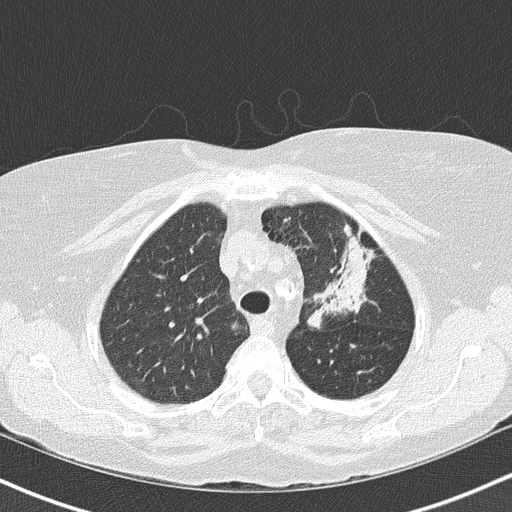
Low-dose screening chest CT, one axial slice; slice 117 of 147 in the series (ordered by position); reconstruction kernel B50f; lung window (W 1500 / L -600 HU); 2 mm slice thickness; 512 × 512 image matrix, field of view 320 × 320 mm.
Structures marked on this image (manually delineated by an expert):
- lesion 1 (tumor, upper lobe of left lung): bounding box <327,238,368,312> (left, top, right, bottom; pixels)